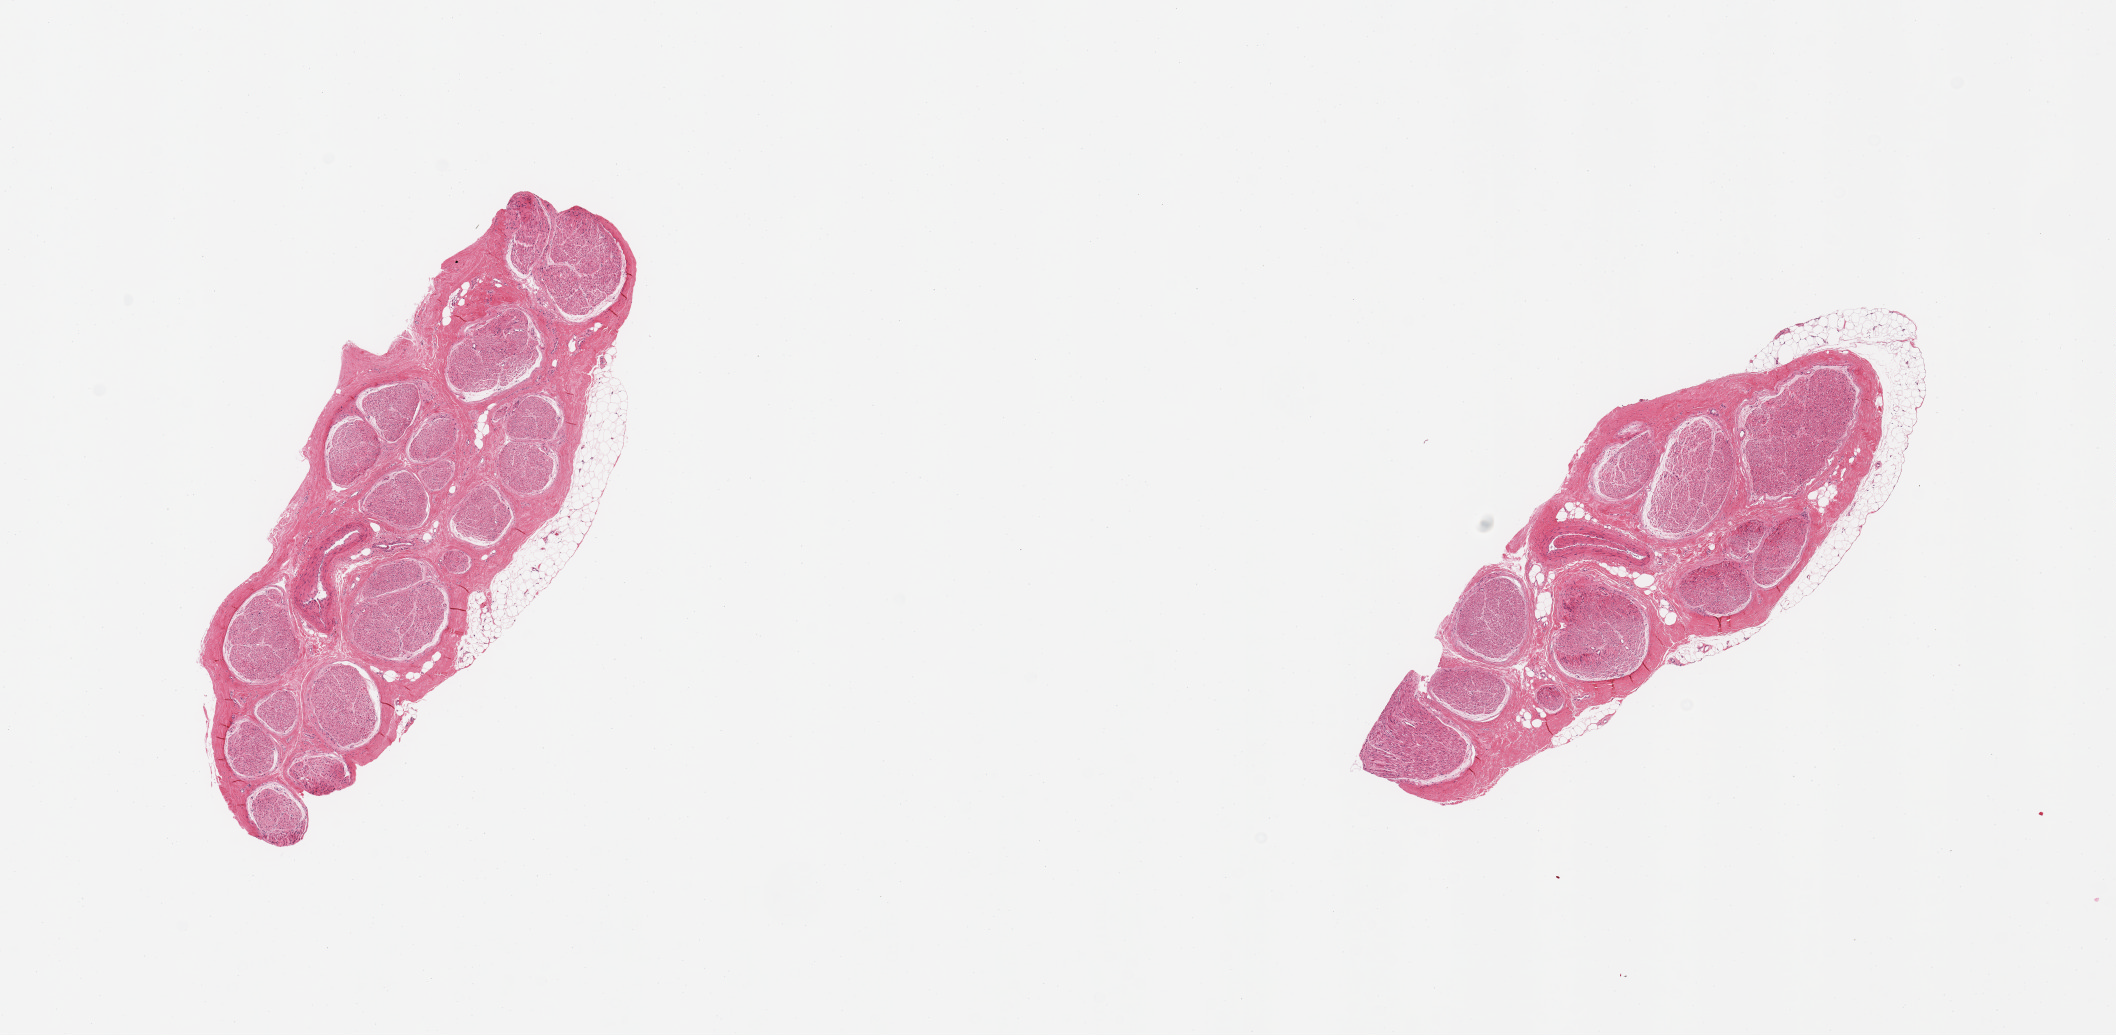
Hematoxylin and eosin (H&E) whole-slide image — low-resolution overview of the scanned area, about 16.7 x 8.2 mm (slide scanned at 20x), PAXgene-fixed, paraffin-embedded tissue, target tissue: tibial nerve, tissue donor sample. Donor: male.
• reviewer comment on this tissue sample: 2 pieces, nubbins of adherent fat up to ~0.5mm